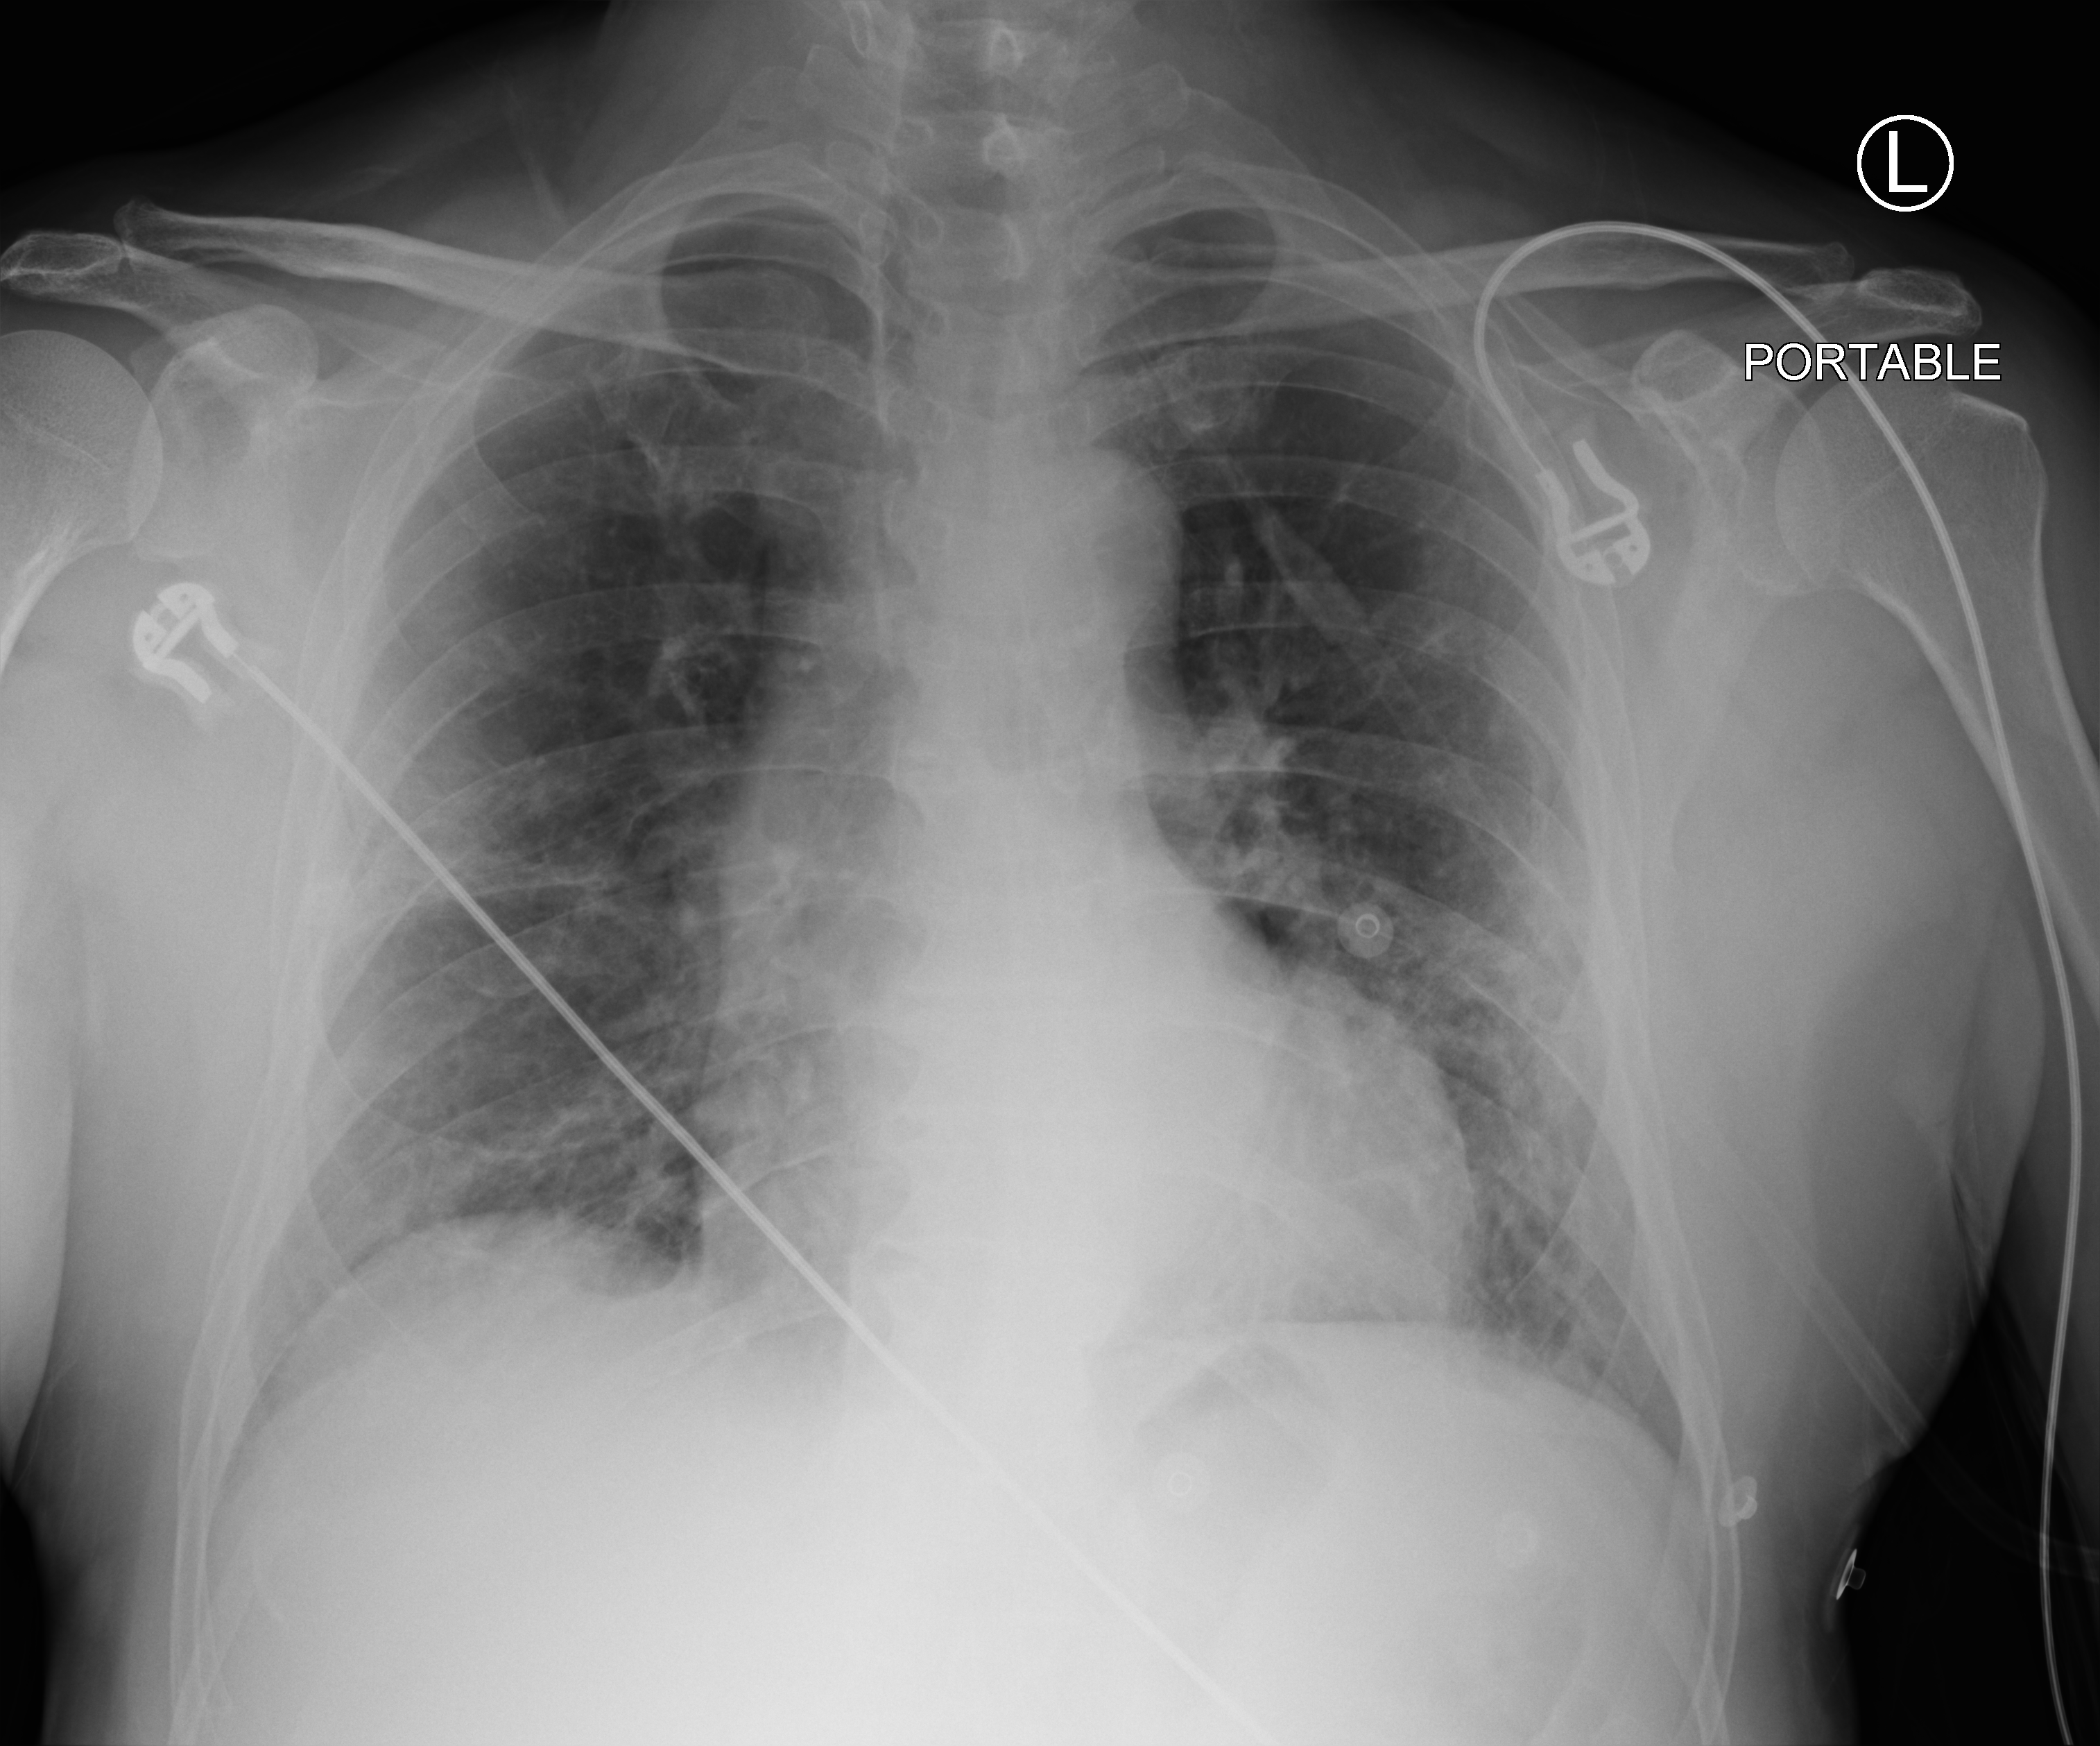
Portable chest radiograph; anteroposterior (AP) projection. Patient hospitalised with COVID-19; male, aged 60–74 years.
Admission-level facts for this patient (not findings on this image; timing relative to this image not recorded):
- admitted to intensive care during this hospital stay: no
- other chronic lung disease (admission record): no
- mechanically ventilated during this hospital stay: no